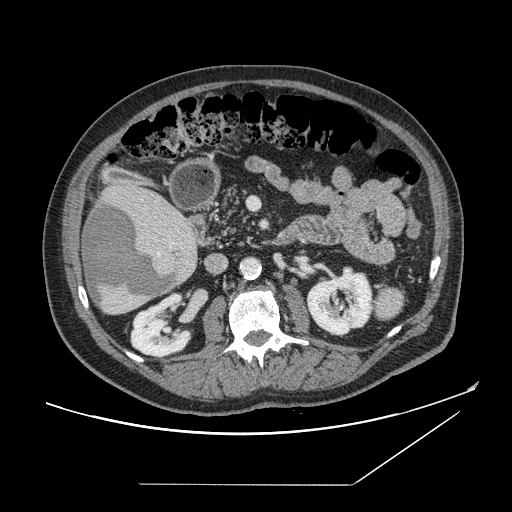
Contrast-enhanced abdominal CT, one axial slice; position 65 of 166 along the scan axis; 120 kVp; intravenous contrast given; soft-tissue window (W 400 / L 40 HU); 2.5 mm slice thickness; 512 × 512 image matrix, field of view 416 × 416 mm. Male patient, age 80 years. From the clinical record (not read from this slice): diagnosis: colorectal cancer liver metastases, imaged before liver resection; multiple liver metastases: no; largest metastasis: 2.2 cm; chemotherapy before resection: no.
Outlined on this slice (manually delineated by an expert):
- liver: bounding box [x1, y1, x2, y2] px = [81, 184, 199, 315]
- planned liver remnant (the part of the liver to remain after resection): [121, 186, 176, 212]
- liver metastasis: [84, 203, 179, 307]